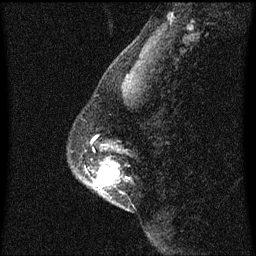
Breast MRI (dynamic contrast-enhanced), one sagittal slice. Slice 17 of 60 in the series (ordered by position). Dynamic contrast-enhanced series, image 2 of 3 at this slice position (ordered by acquisition). 1.5 T. TE 4.2 ms, TR 8.4 ms. 256 × 256 image matrix. Patient: female, 40 years. From the clinical record (not read from this slice): setting: breast cancer imaged before/during neoadjuvant chemotherapy; receptor status: triple-negative.
Outlined on this slice (semi-automatic segmentation, software-assisted and operator-edited):
- analysis volume of interest (the breast-tissue region the enhancement analysis was run in; not a lesion): bounding box <78,146,129,211> (left, top, right, bottom; pixels)
- tumour enhancement mask (voxels above the 70 % enhancement threshold inside the analysis volume of interest): <96,162,119,187>